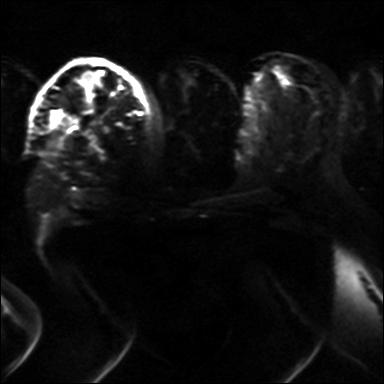
Breast MRI, one axial slice. Diffusion-weighted series; image 2 of 4 stored at this slice position (different b-values; order by instance number). 3 T. 4 mm slice thickness. 384 × 384 image matrix, field of view 320 × 320 mm. Female patient.
Outlined on this slice (expert manual segmentation):
- tumour on diffusion-weighted imaging: box from (x=58, y=110) to (x=68, y=117) px